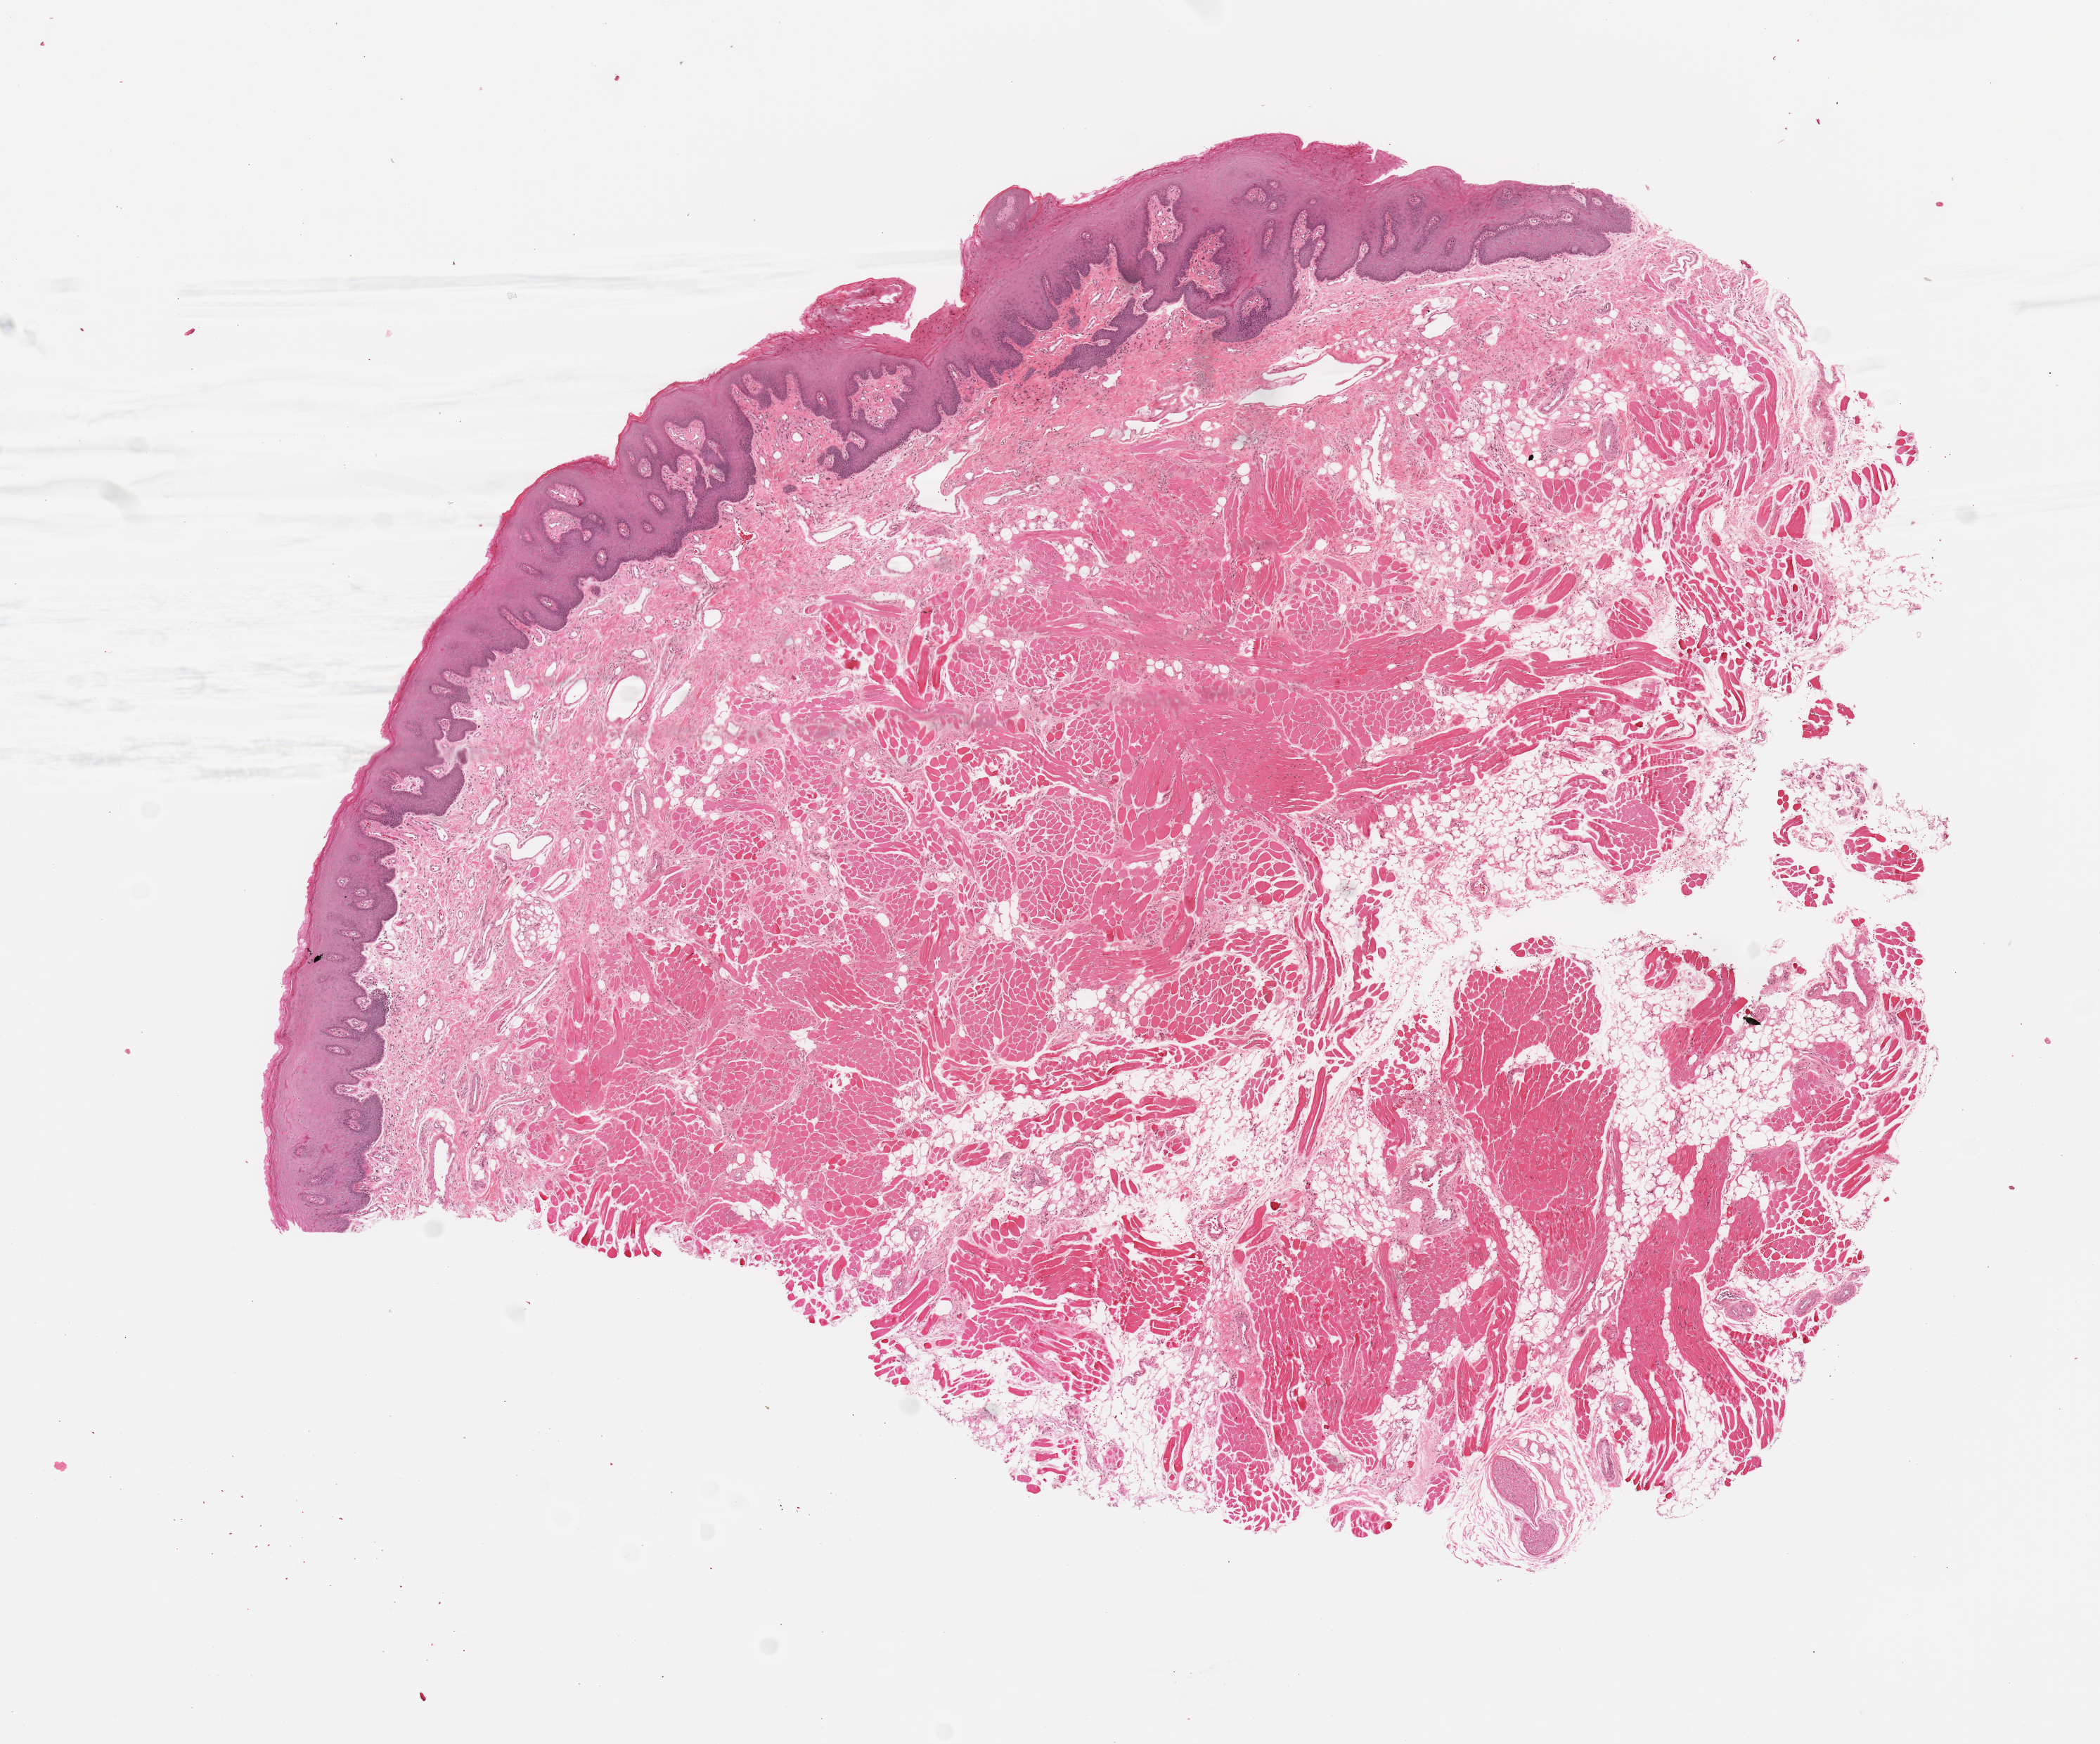
Whole-slide histology image, Hematoxylin and eosin (H&E) stained — a low-resolution overview of the entire scanned area, about 11.8 x 9.8 mm; normal (non-tumour) tissue sample, sampled site: floor of mouth. Male, 57 y/o.
This section: normal (non-tumour) tissue from the same patient. Patient diagnosis: Squamous cell carcinoma, NOS.